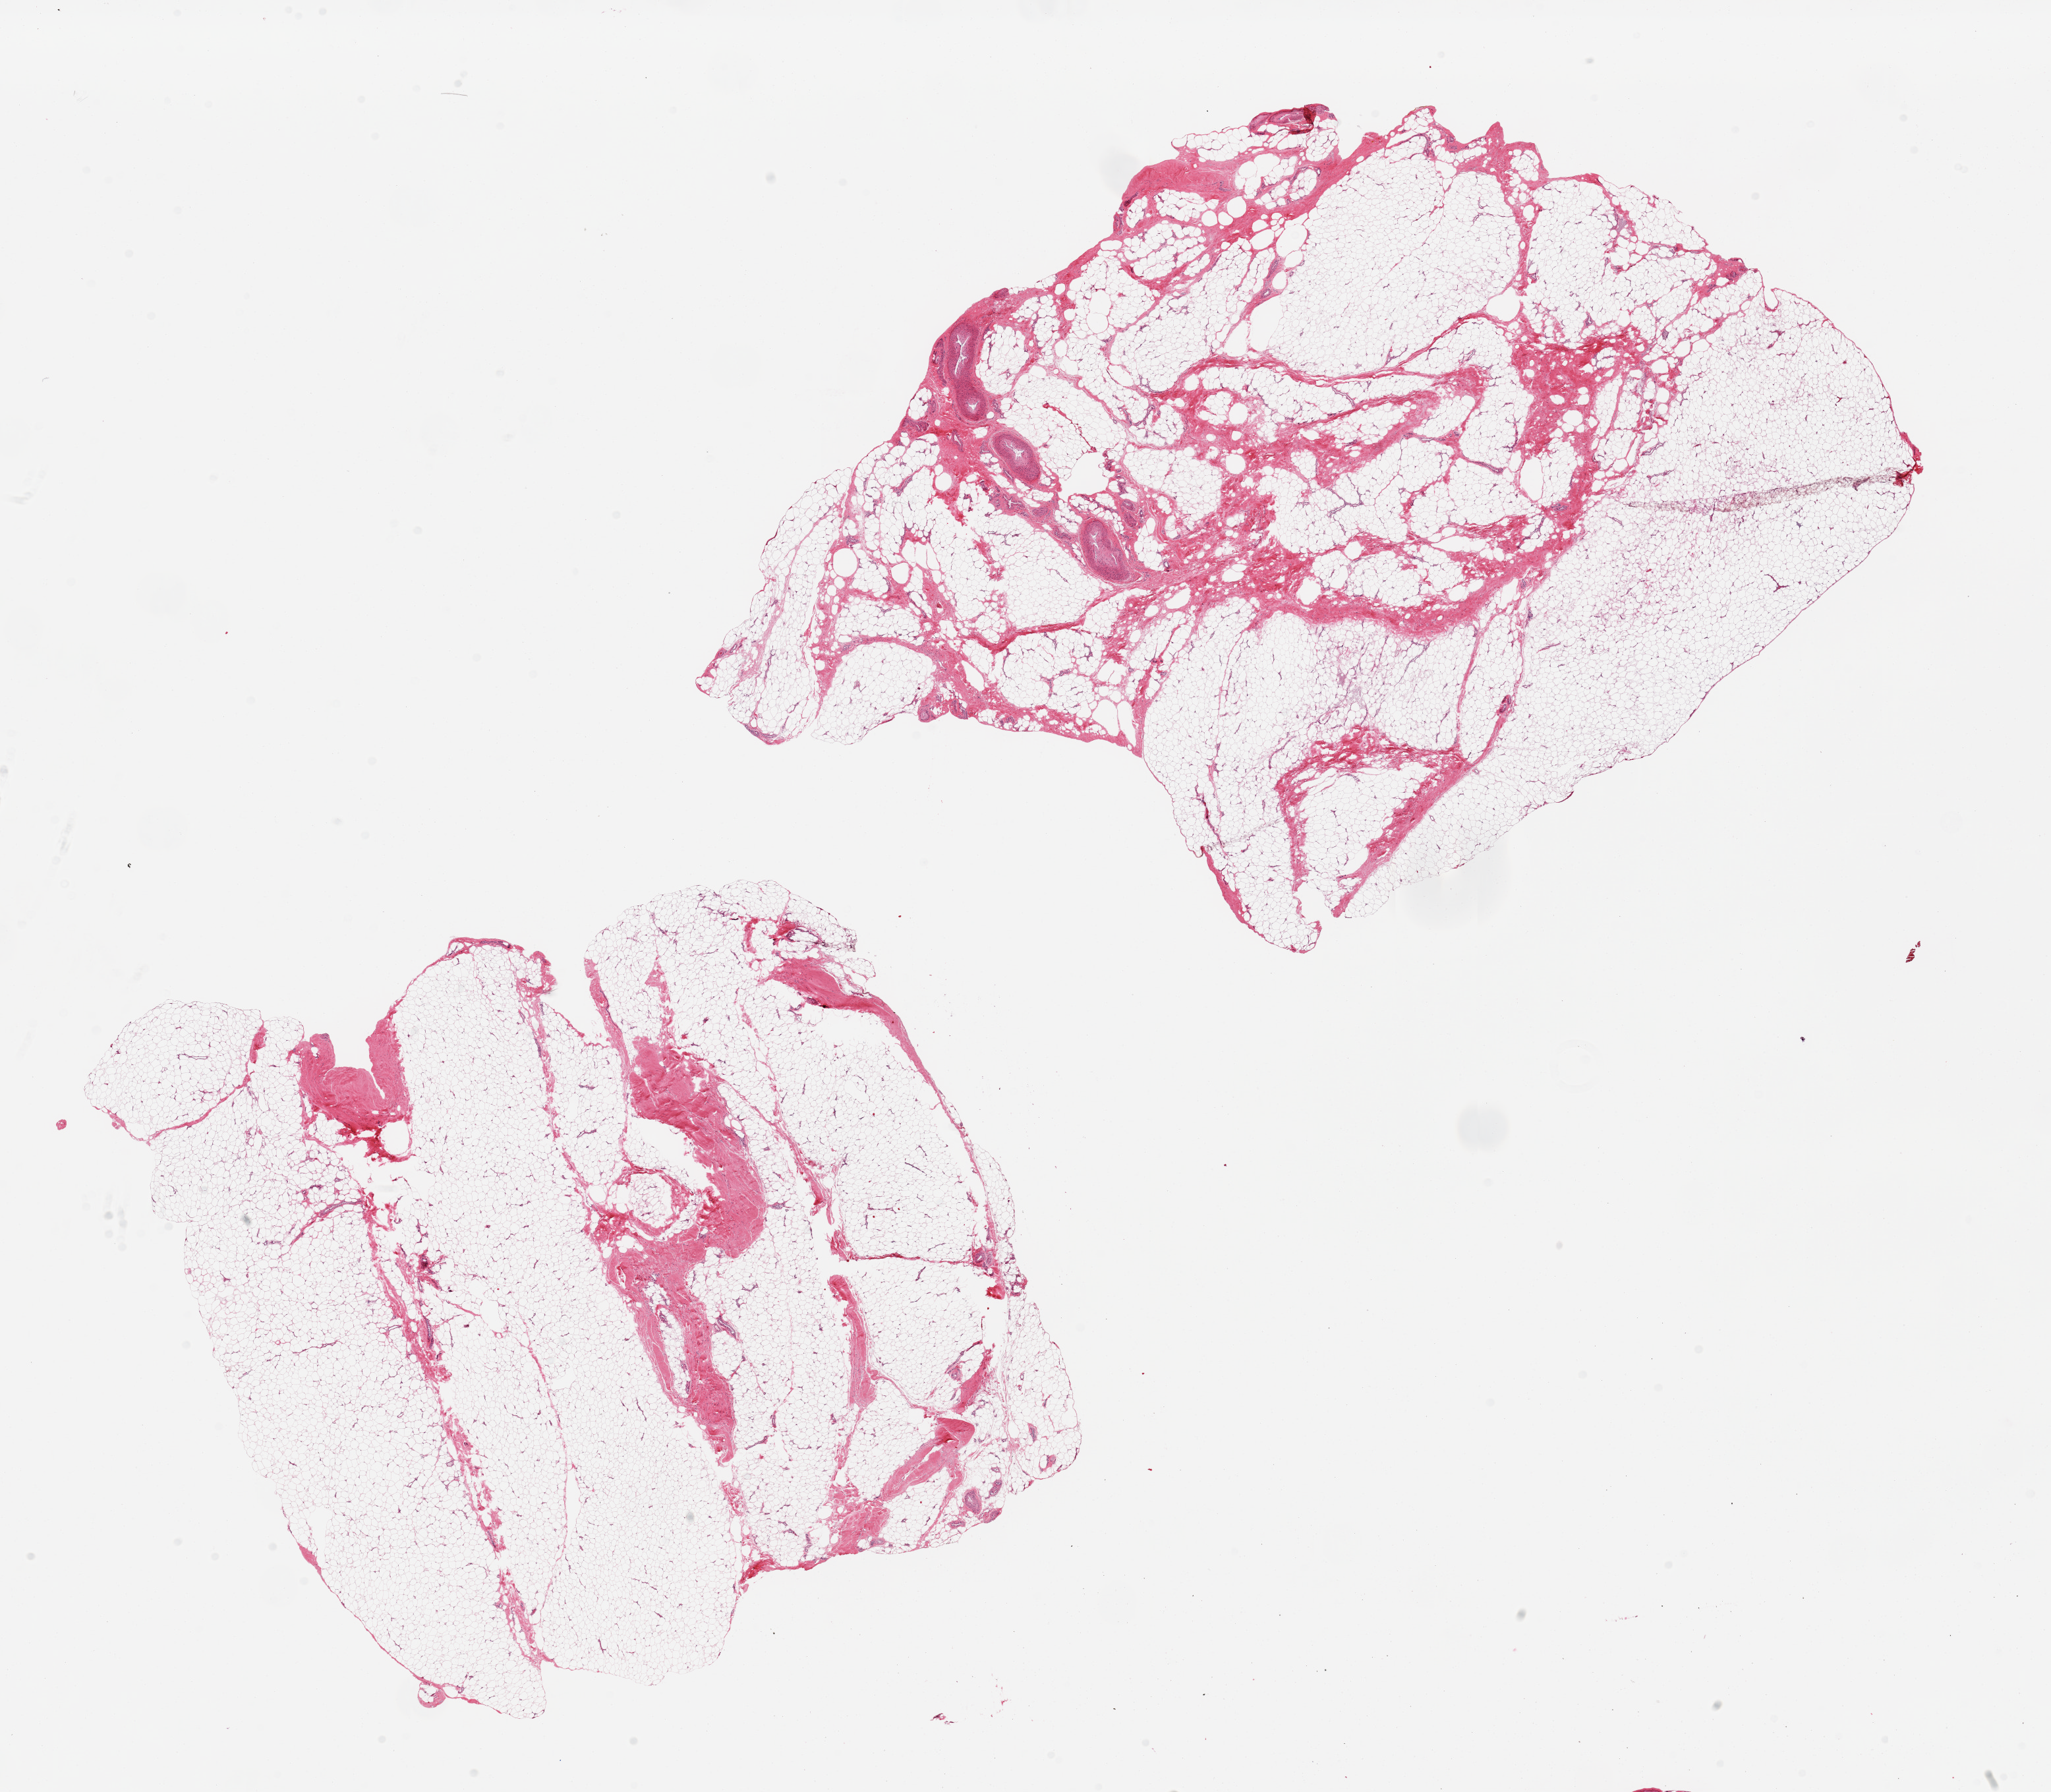
Whole-slide image, hematoxylin and eosin (H&E) stain, shown as a low-resolution overview of the whole scanned area (about 24.6 x 21.5 mm); PAXgene-fixed, paraffin-embedded tissue; section of adipose tissue (target tissue); tissue donor sample.
Review note (as recorded): 2 pieces; 10 & 20% fibrovascular content.